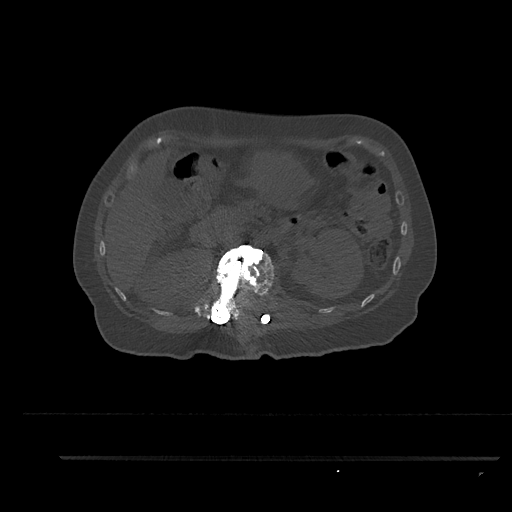
CT including the spine, one axial slice. Position 223 of 797 along the scan axis. Reconstruction kernel Br40s/3. 120 kVp. Bone window (W 1800 / L 400 HU). 0.5 mm slice thickness. 512 × 512 image matrix, field of view 408 × 408 mm. Female patient, age 44 years. From the clinical record (not read from this slice): primary cancer: renal; vertebrae with lytic lesions (as recorded): L1.
Annotated regions visible in this slice (semi-automatic segmentation, software-assisted and operator-edited):
- L1 vertebra: bounding box [x1, y1, x2, y2] px = [207, 245, 275, 321]
- T12 vertebra: [244, 331, 246, 334]